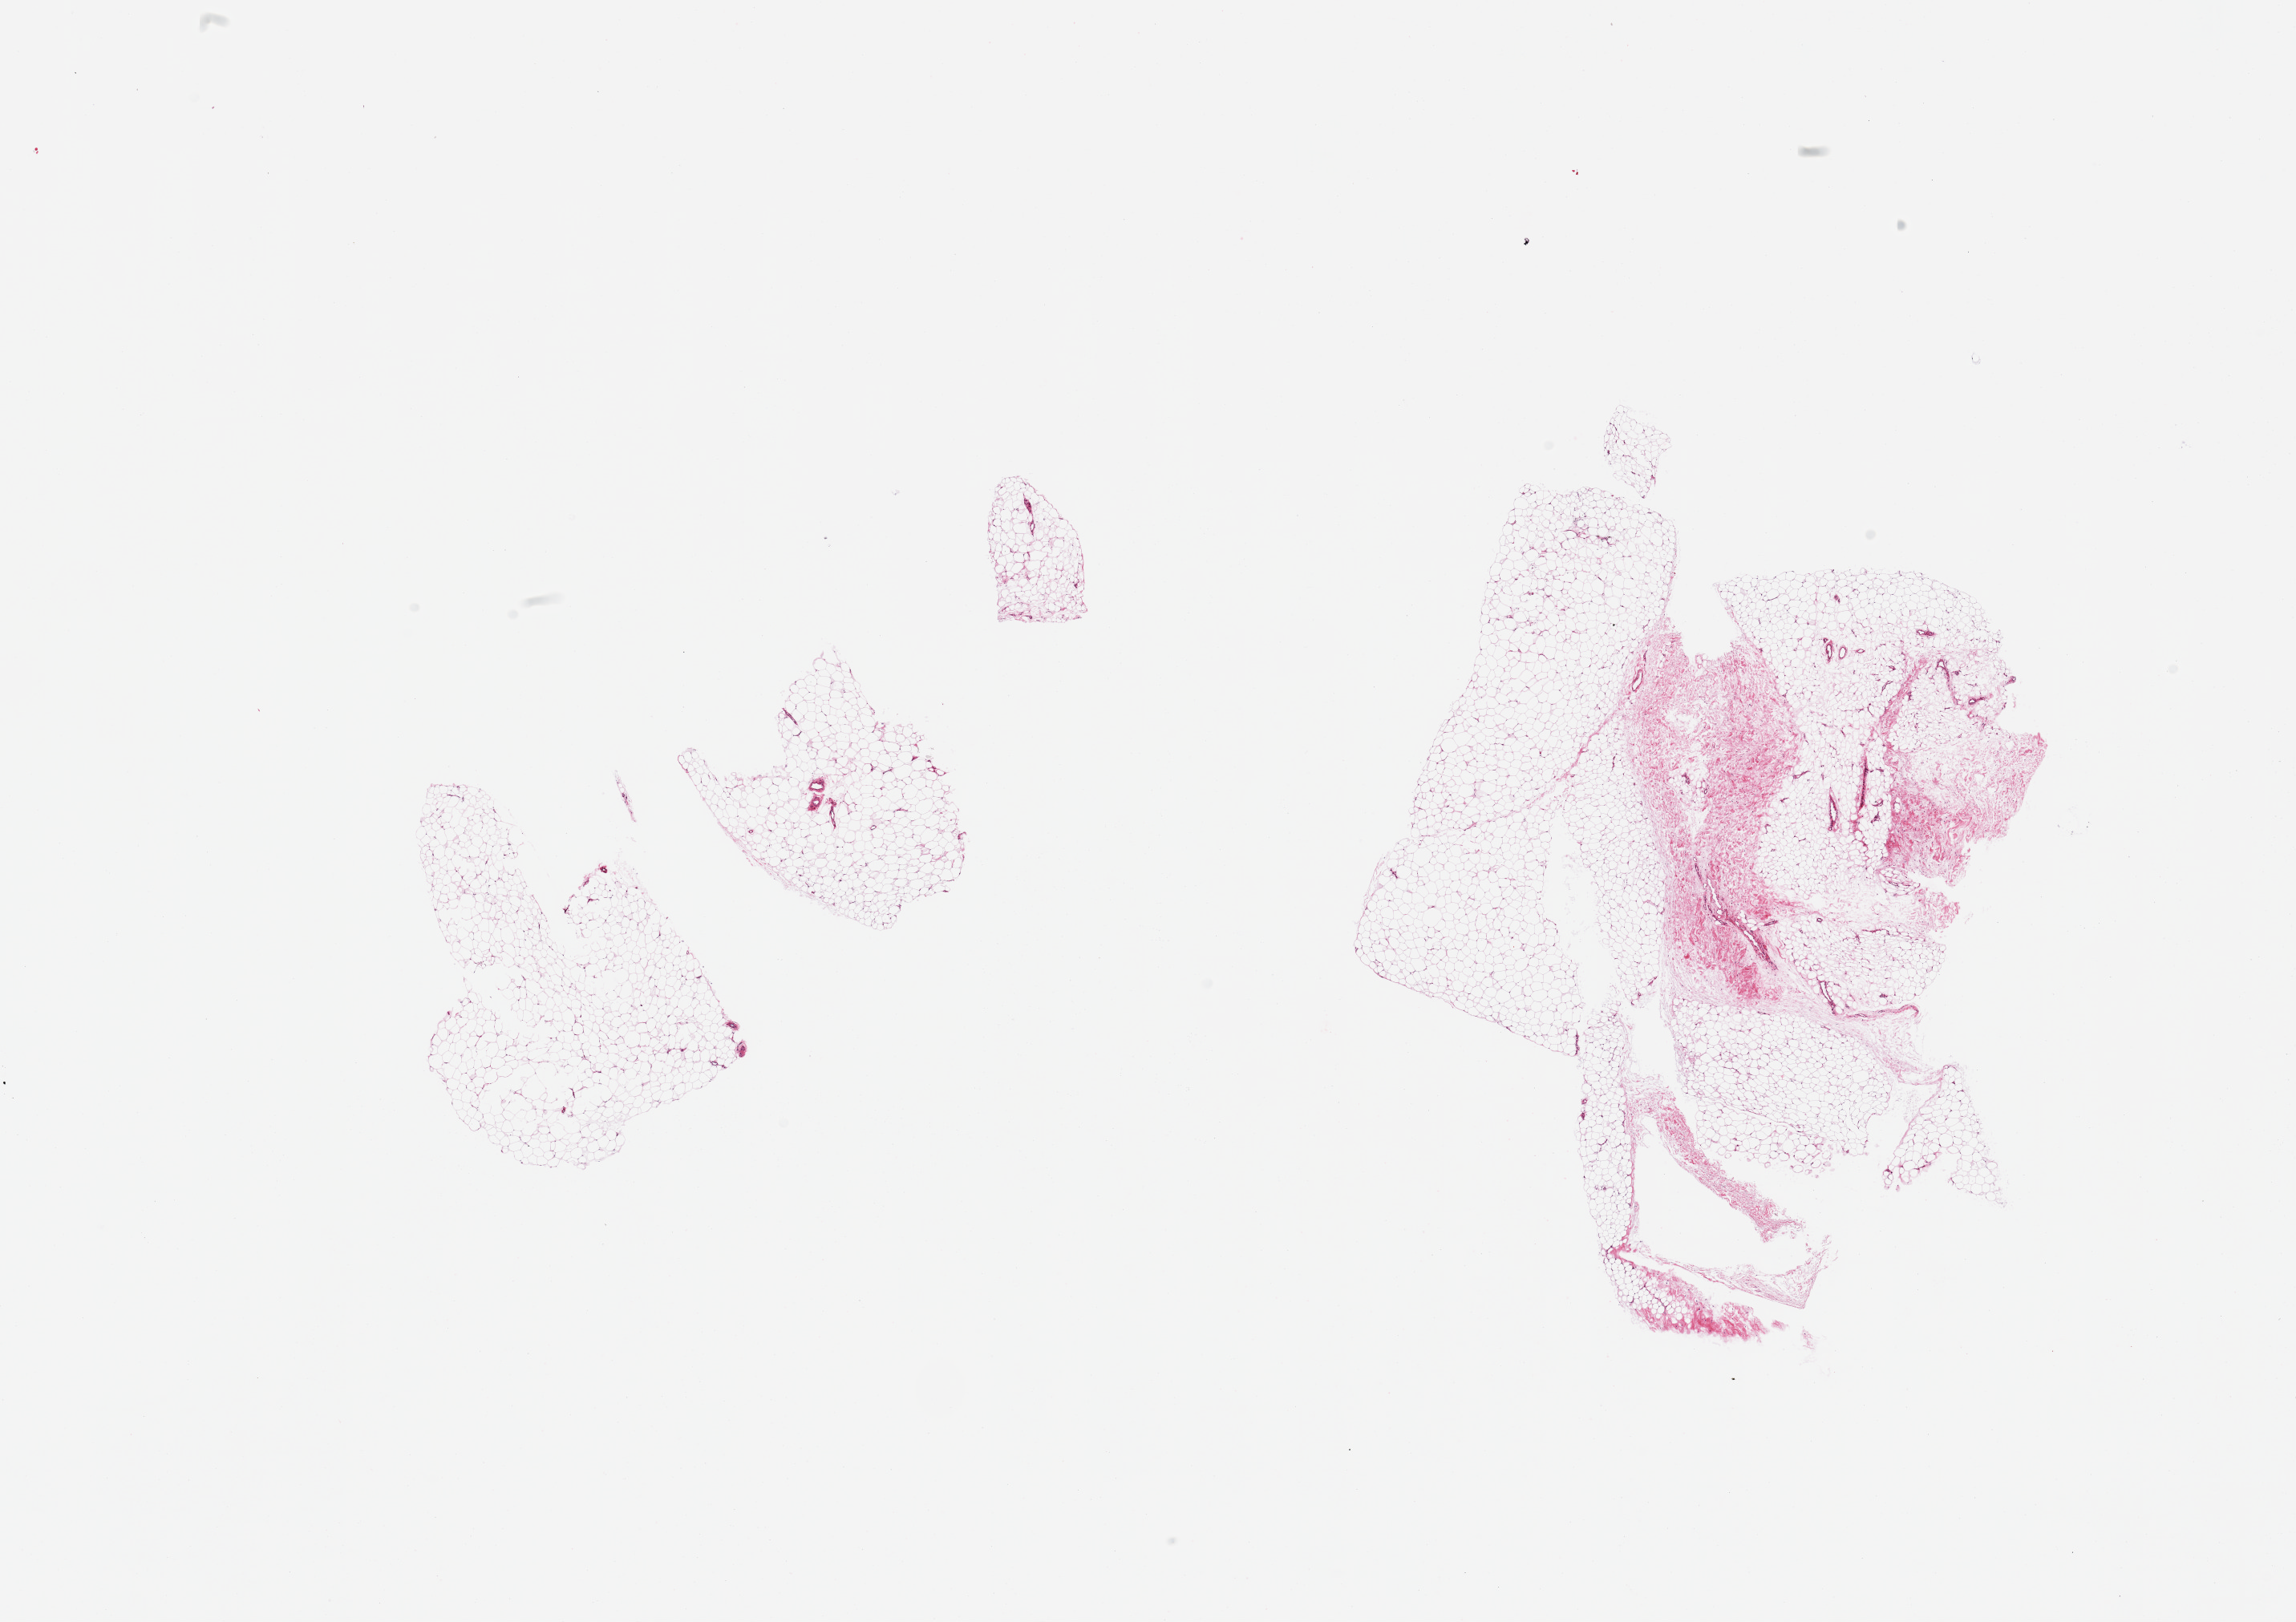
Digitized hematoxylin and eosin (H&E)-stained section, low-resolution overview of the scanned area, about 22.6 x 16.0 mm, PAXgene-fixed paraffin-embedded (PFPE) section, section of adipose tissue (target tissue), donor tissue sample. Female donor.
• pathologist's review note for this sample: 2 pieces, 10-15% fascia